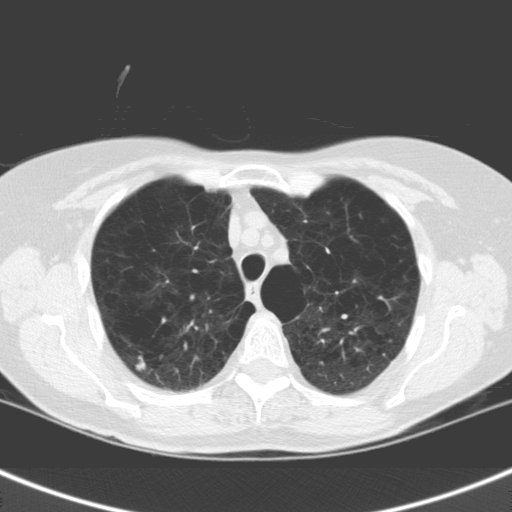
Low-dose screening chest CT, axial slice; second screening round (one year after baseline); lung window (W 1500 / L -600 HU); standard (soft-tissue) reconstruction kernel (C); 120 kVp; slice 39 of 158 in the series; 512 × 512 image matrix. Female participant, aged 63 years at enrolment.
Lesion marked by an expert reader, bounding box (x1, y1, x2, y2) in pixels: (117, 341, 160, 388). The exam's reader record, not a measurement of the box and not confirmed to be the same lesion: non-calcified nodule or mass ≥4 mm, right upper lobe, 7 × 7 mm, spiculated (stellate) margins, soft tissue attenuation, pre-existing on the prior screen: no. Official screen result: positive, other. Later outcome: lung cancer diagnosed 228 days after this screen — squamous cell carcinoma, NOS, right upper lobe, moderately differentiated (G2), stage IA (AJCC 6th edition), 14 mm at pathology.